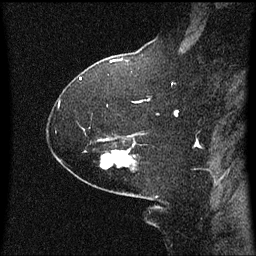
Breast MRI (dynamic contrast-enhanced), one sagittal slice. Position 41 of 60 along the scan axis. Dynamic contrast-enhanced series, image 2 of 3 at this slice position (ordered by acquisition). 1.5 T. TE 4.2 ms, TR 8 ms. 2.1 mm slice thickness. 256 × 256 image matrix, field of view 200 × 200 mm. Patient: female, 59 years.
Outlined on this slice (semi-automatic segmentation, software-assisted and operator-edited):
- analysis volume of interest (the breast-tissue region the enhancement analysis was run in; not a lesion): bounding box <86,142,137,171> (left, top, right, bottom; pixels)
- tumour enhancement mask (voxels above the 70 % enhancement threshold inside the analysis volume of interest): <112,150,119,157>